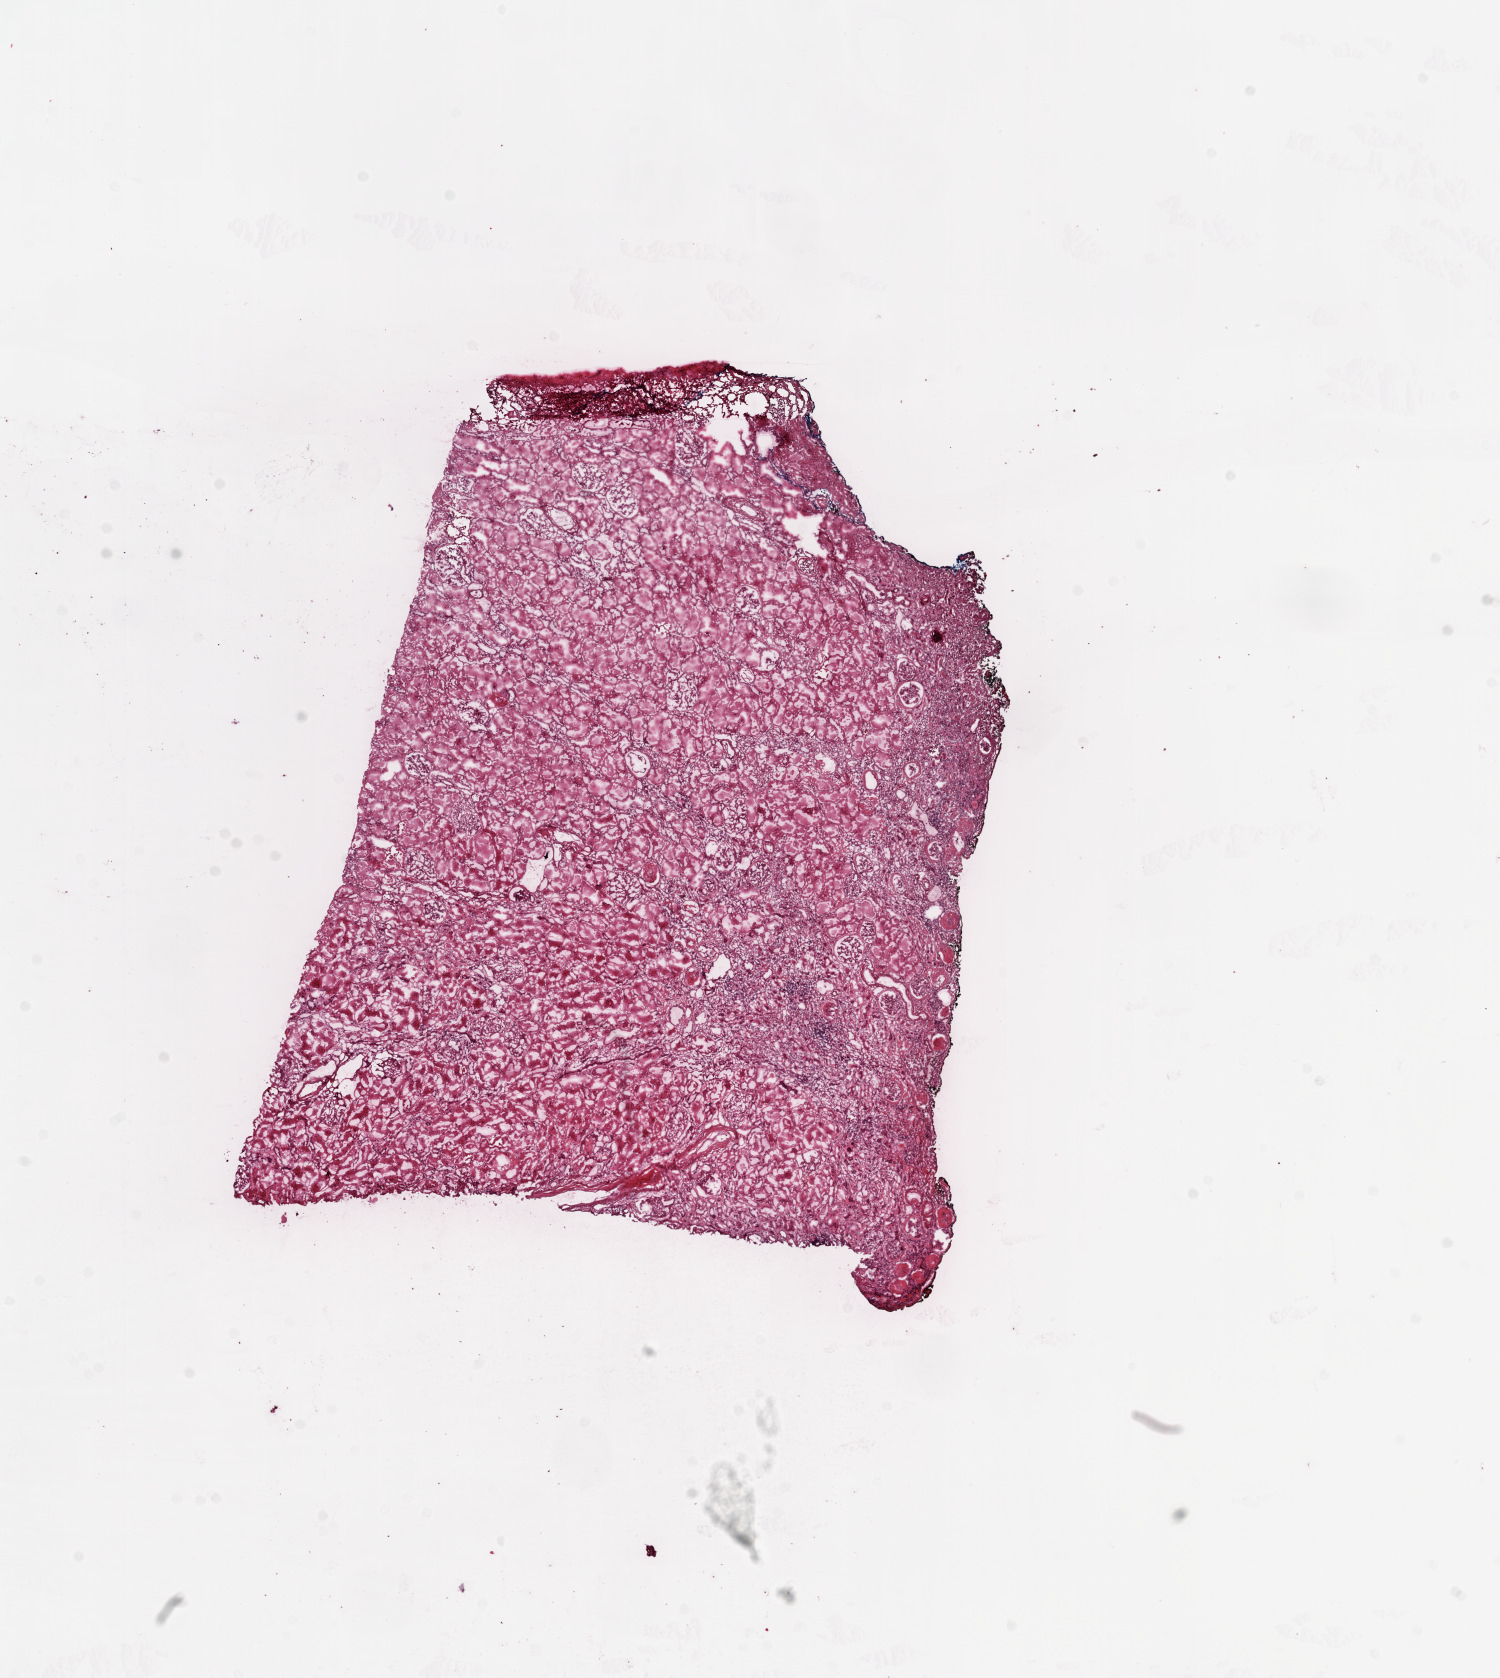
Digitized H&E tissue section (whole slide), whole scanned area (about 12.0 x 13.5 mm, acquisition: 20x scan) shown as a low-resolution overview, frozen section, solid tissue normal (non-tumour tissue) sample from the kidney. Female, age 55 years at initial diagnosis.
• this section: solid tissue normal sample (biorepository sample class)
• patient diagnosis: Clear cell adenocarcinoma, NOS